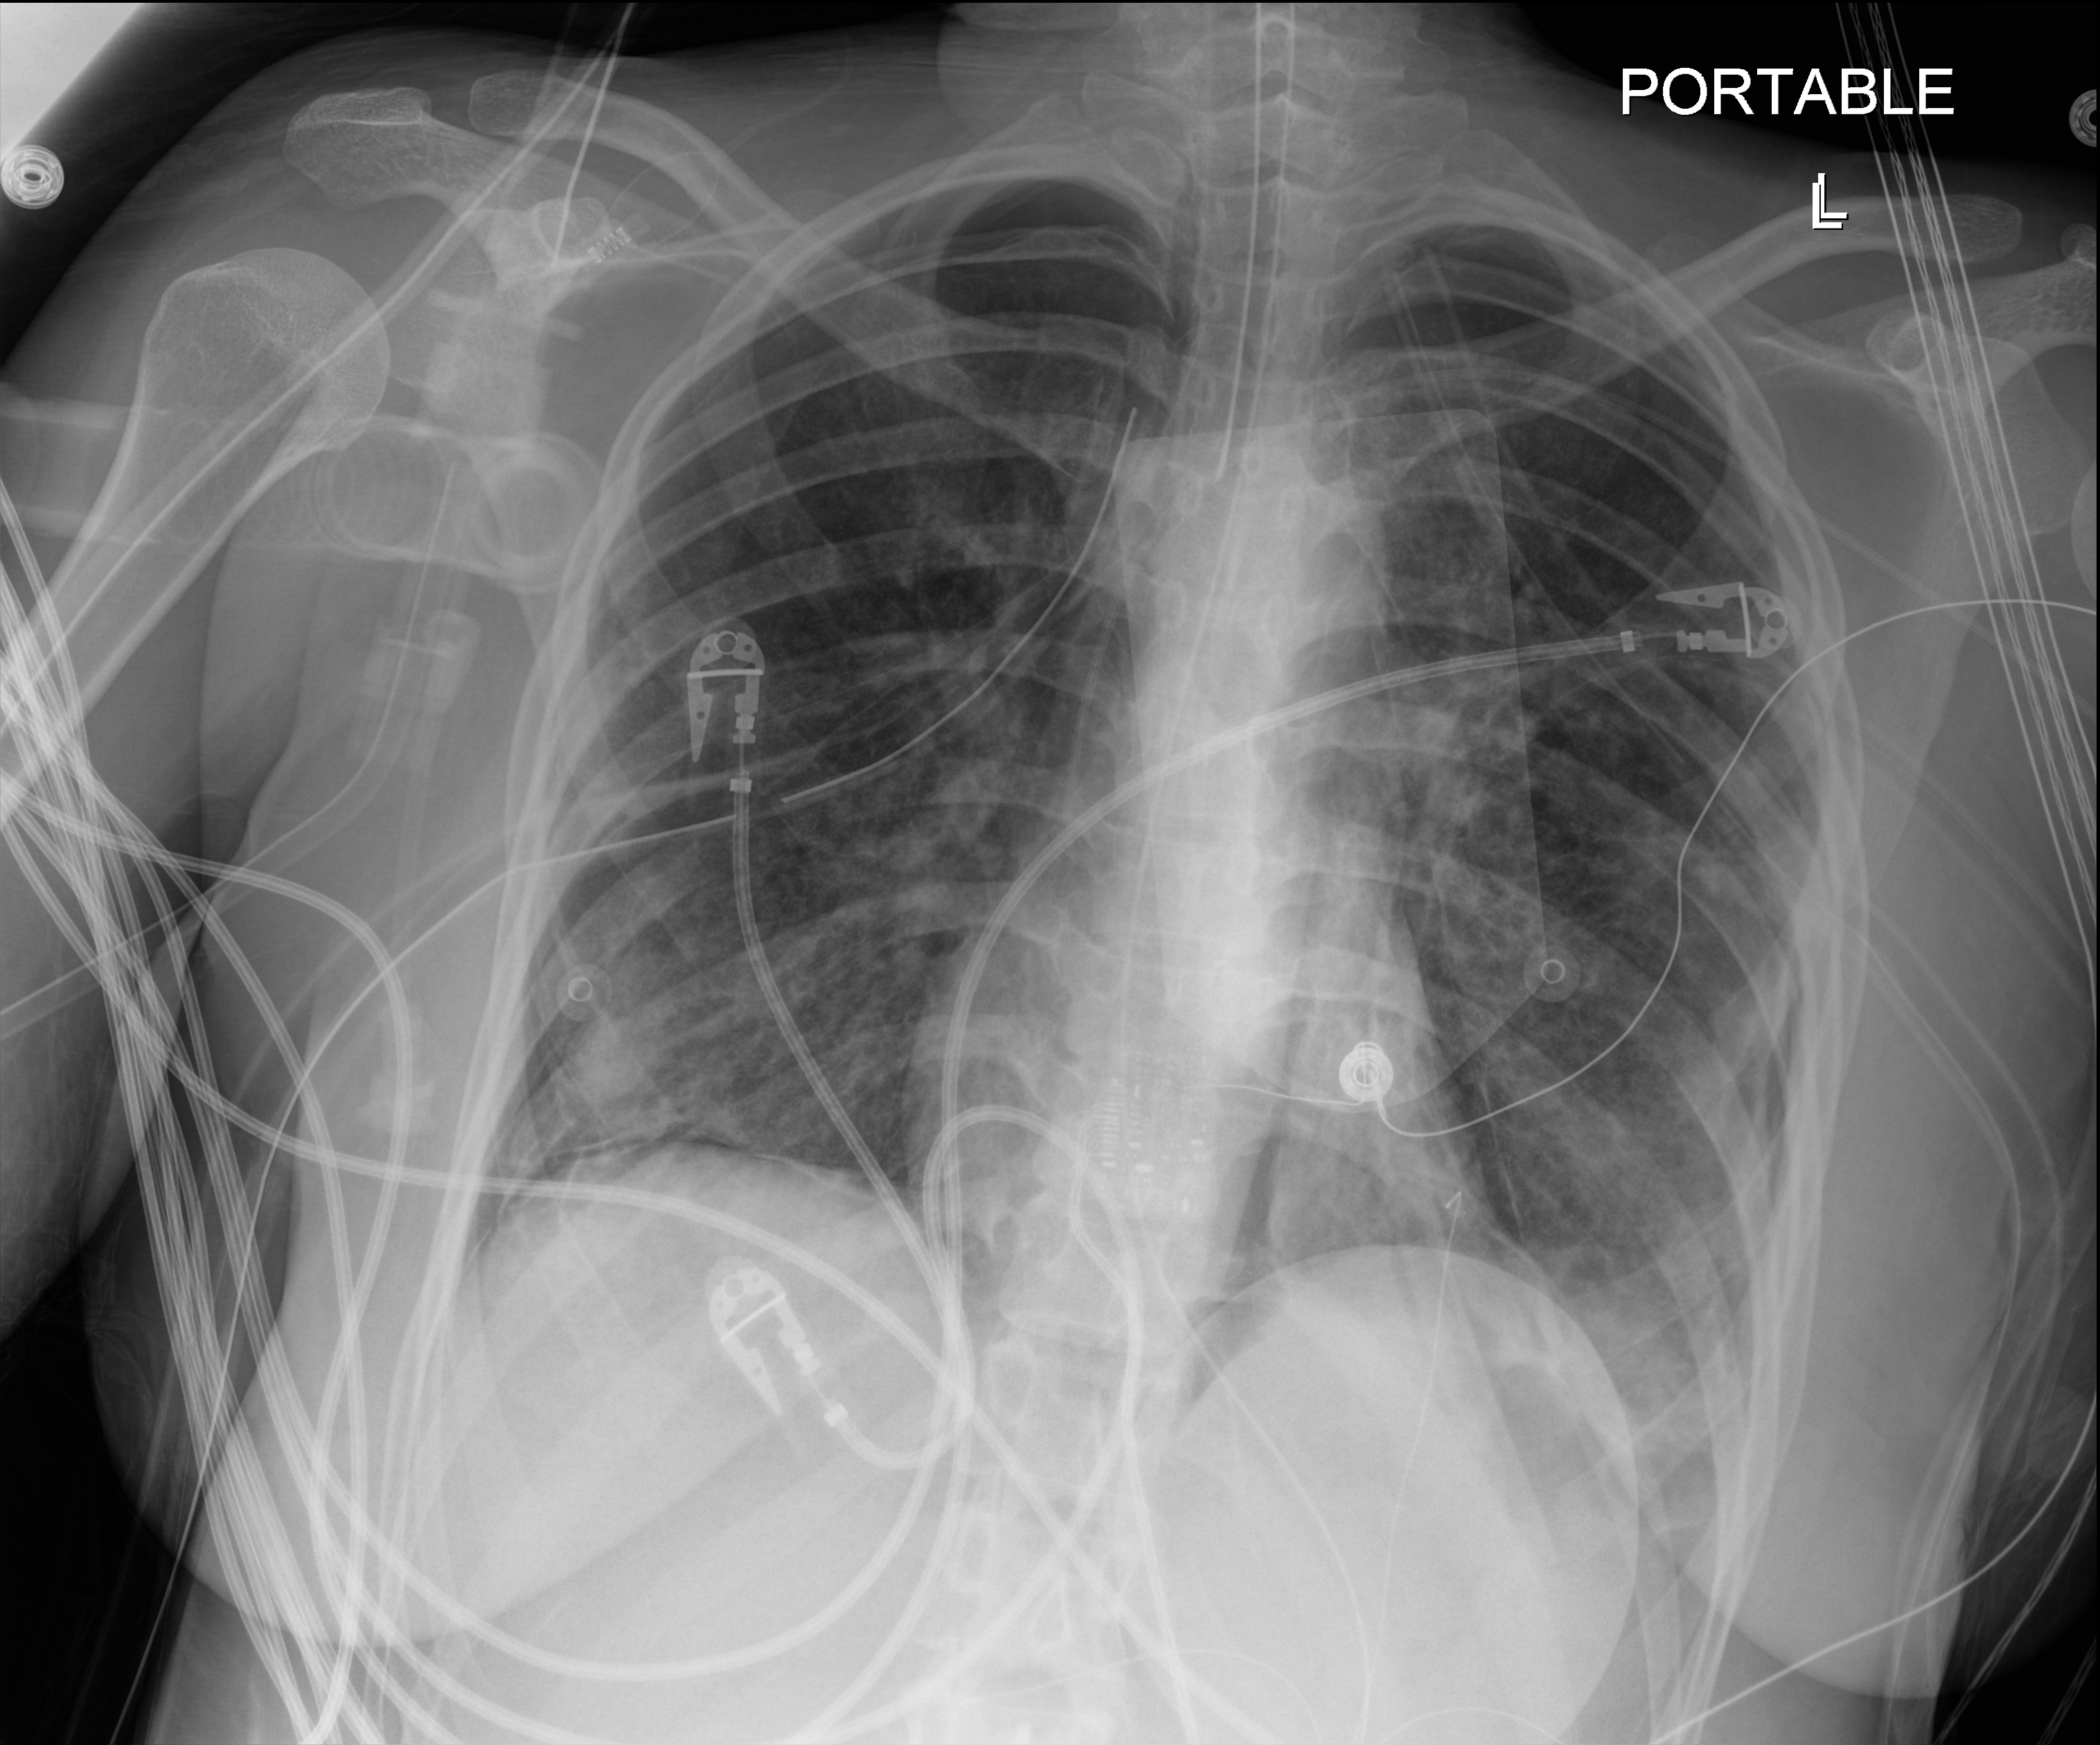
Portable chest radiograph. Patient hospitalised with COVID-19, aged 18–59 years.
Admission-level facts for this patient (not findings on this image; timing relative to this image not recorded): admitted to intensive care during this hospital stay: yes; length of hospital stay: 30 days.